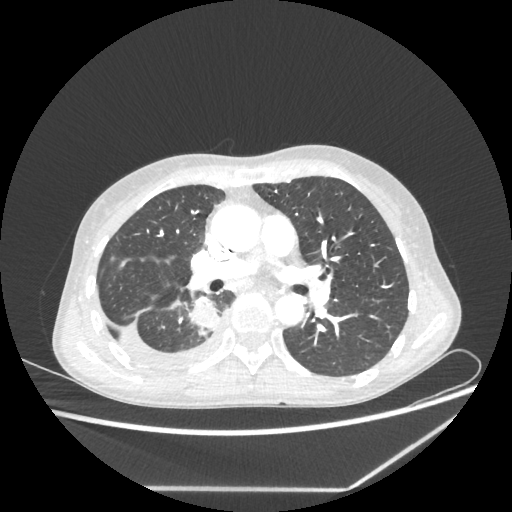
Chest CT, one axial slice. Position 131 of 237 along the scan axis. Reconstruction kernel STANDARD. 80 kVp. Lung window (W 1500 / L -600 HU). 1.25 mm slice thickness. 512 × 512 image matrix, field of view 364 × 364 mm. Patient: female, 59 years. Case-level facts recorded for this patient, not image findings: clinical TNM (as recorded): T1c N1 M1.
Annotated regions visible in this slice (rectangle marked by the reading radiologist):
- lung tumour (recorded histology: adenocarcinoma): bounding box [x1, y1, x2, y2] px = [187, 298, 218, 332]